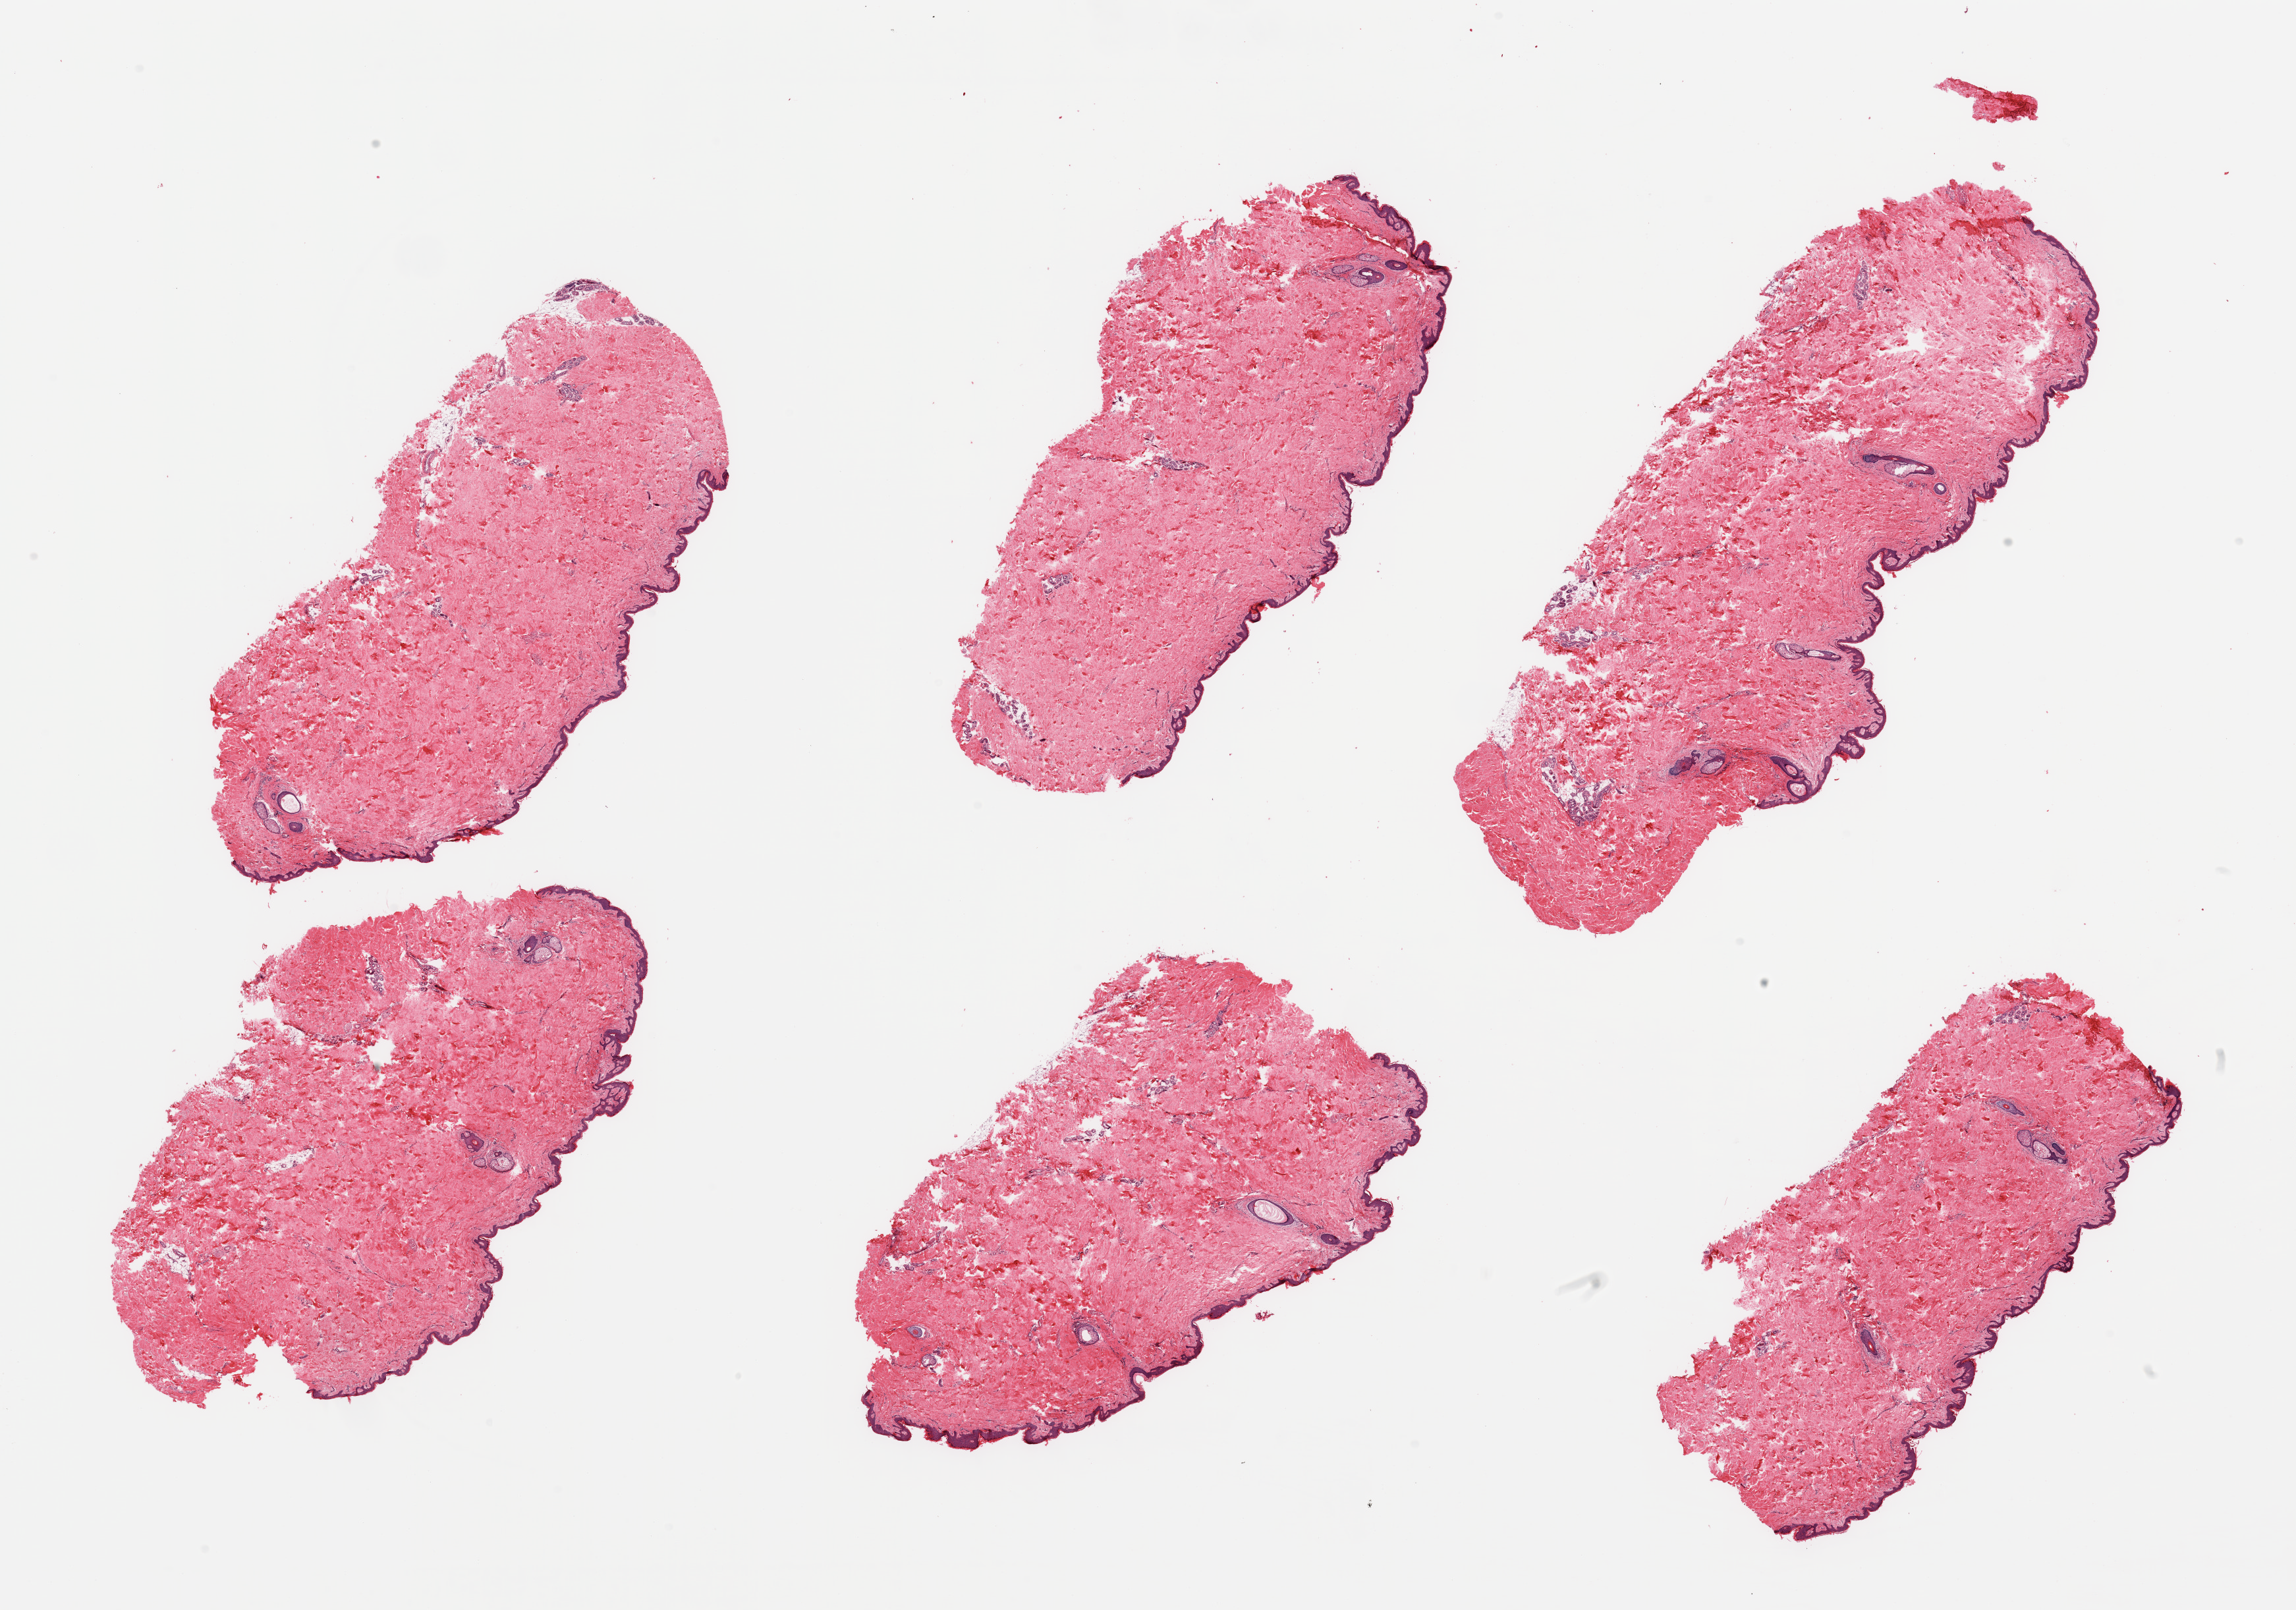
Digitized haematoxylin and eosin-stained section — whole scanned area (about 27.6 x 19.3 mm) shown as a low-resolution overview. PAXgene-fixed paraffin-embedded (PFPE) section. Section of skin of suprapubic region (target tissue). Donor tissue sample. Donor sex: male.
Review note (as recorded): 6 pieces; well trimmed.